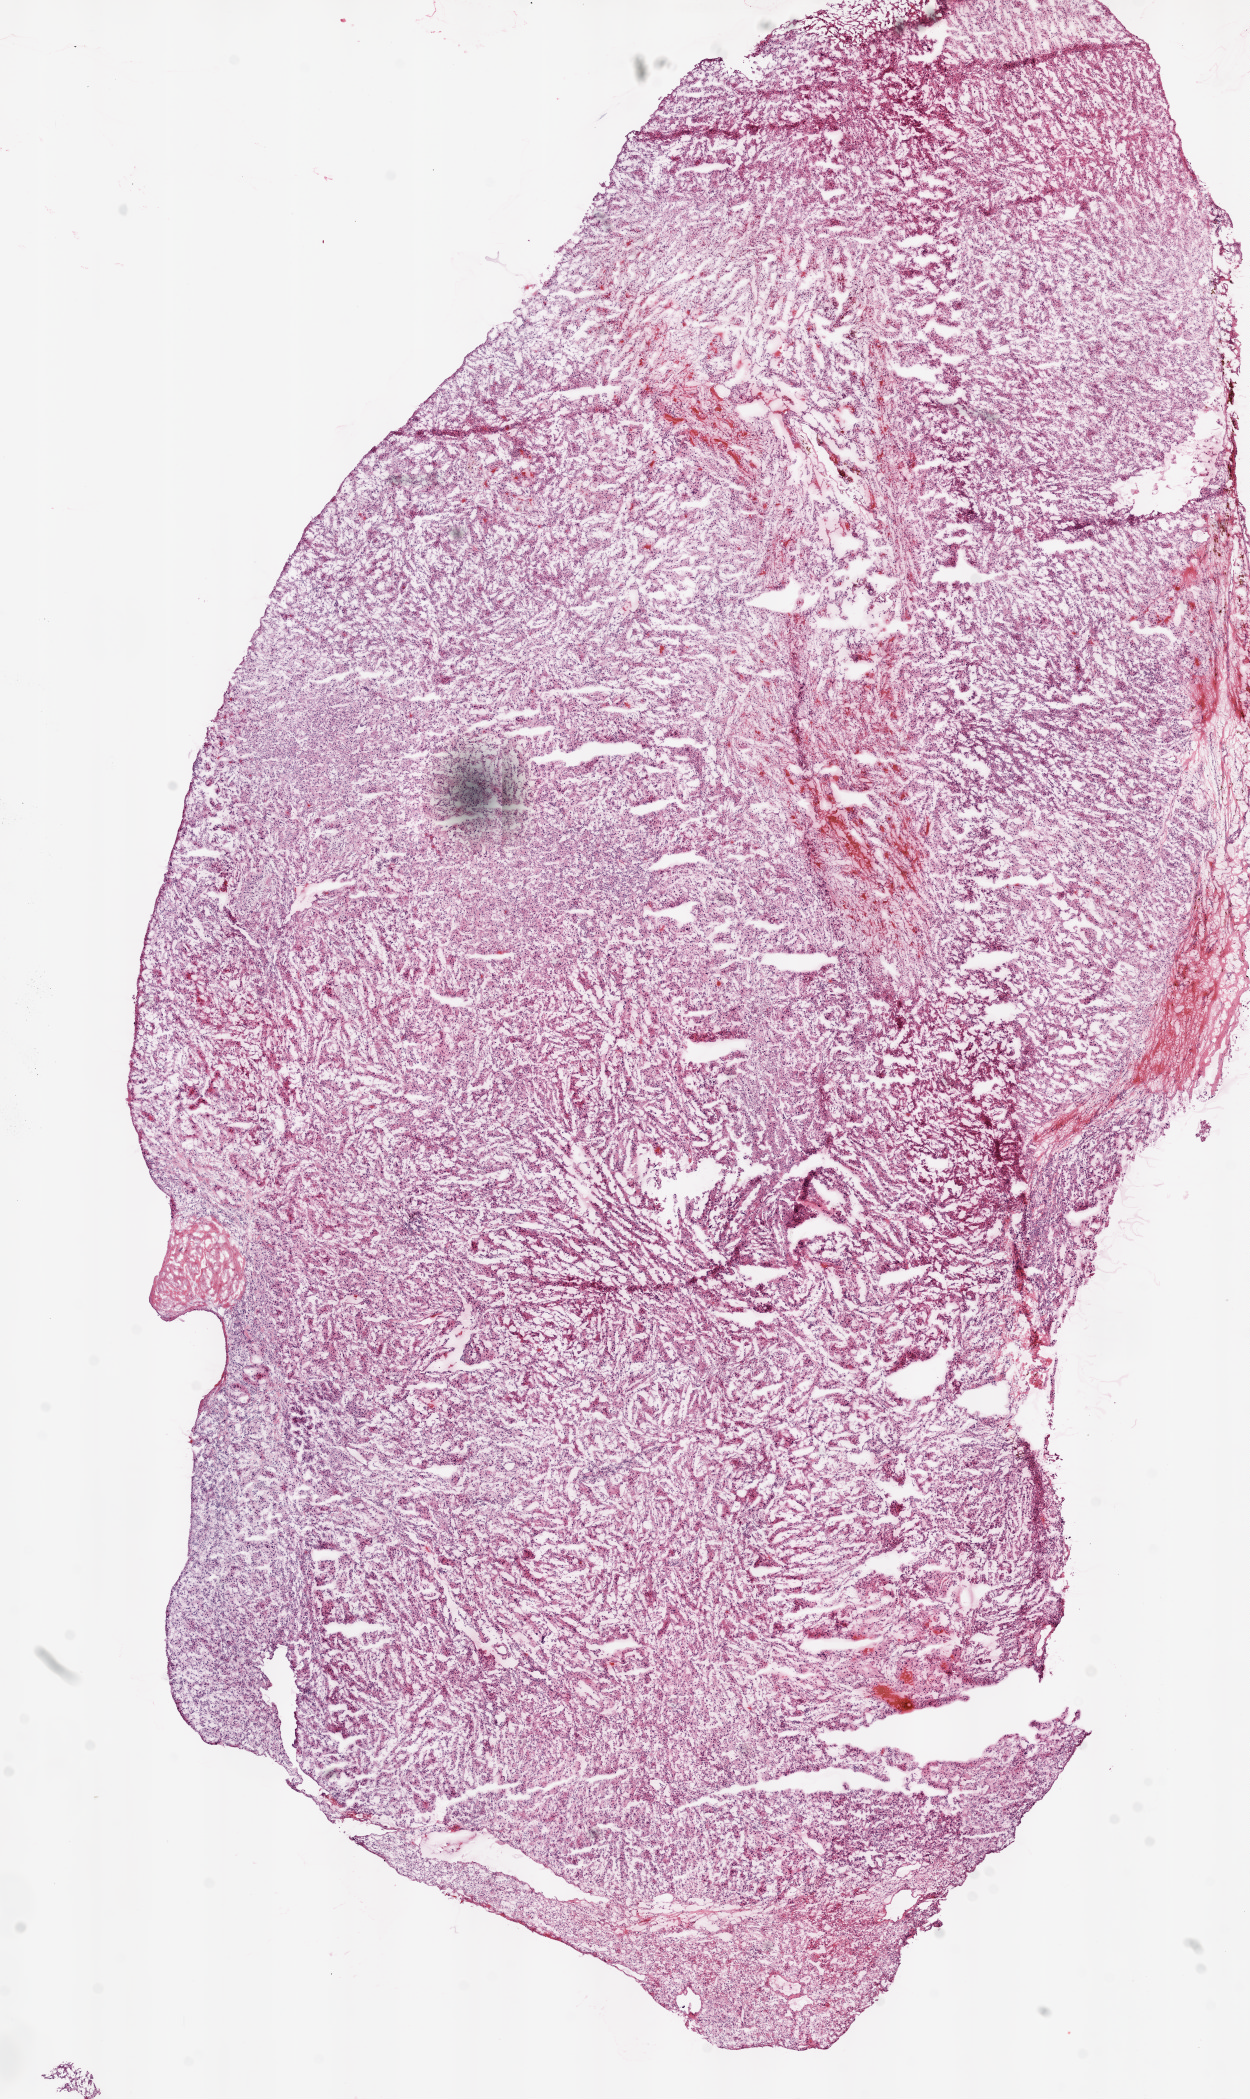
H&E-stained whole-slide image — low-resolution overview of the scanned area, about 10.0 x 16.8 mm (from a 20x scan); frozen section; sample: primary tumour, kidney. Female, age 72 years at initial diagnosis. Slide review estimates, as recorded: tumour cells 95%, tumour nuclei 90%.
Pathologic diagnosis: Clear cell adenocarcinoma, NOS.